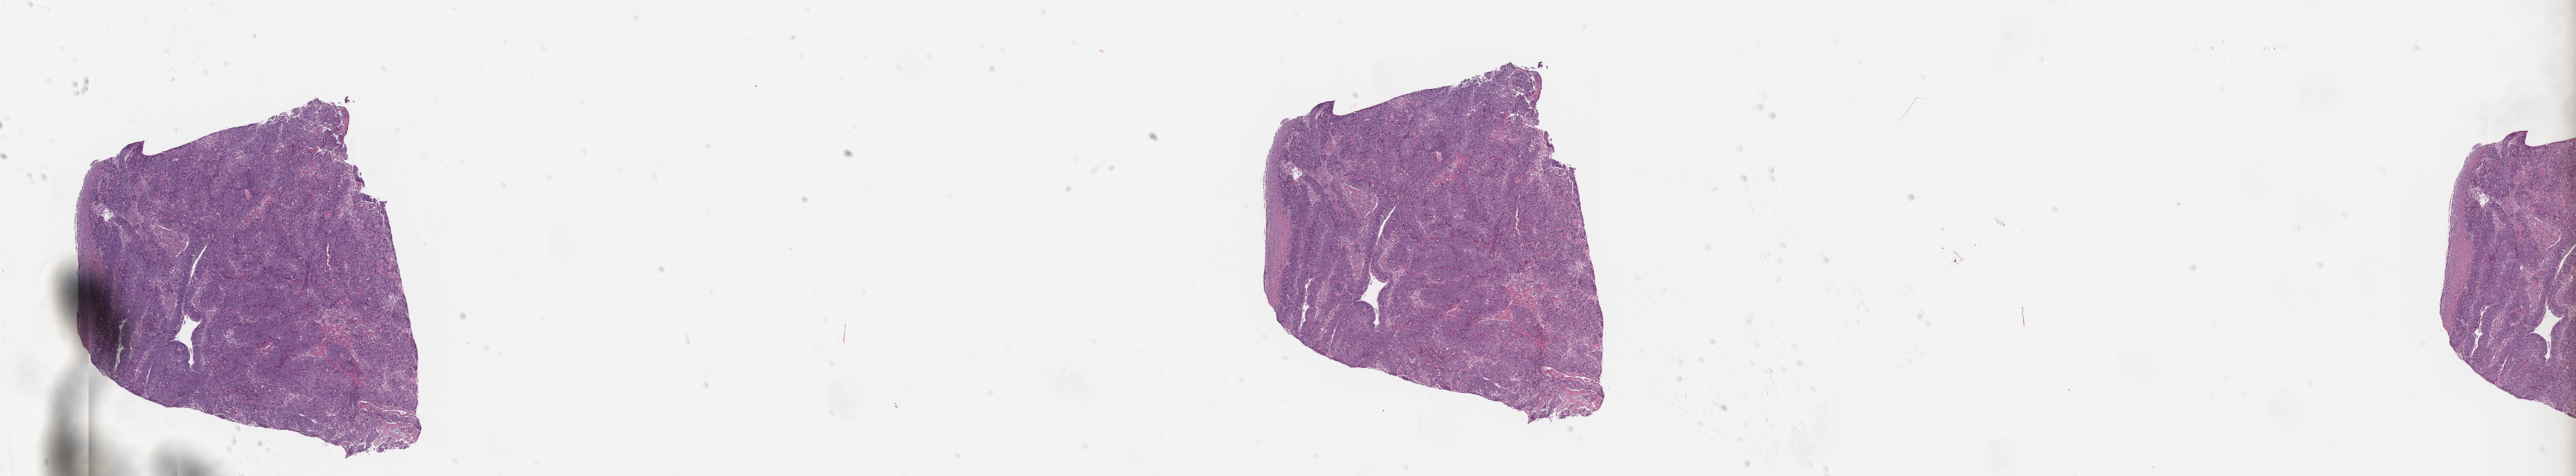
Whole-slide histology image, Hematoxylin and eosin (H&E) stained — shown as a low-resolution overview of the whole scanned area (about 29.0 x 5.4 mm); formalin-fixed paraffin-embedded (FFPE) diagnostic section; primary tumour sample from the uterus. Female patient; age at initial diagnosis 69 years. Histologic grade: G3 (poorly differentiated).
Pathologic diagnosis: Endometrioid adenocarcinoma, NOS (endometrium). FIGO stage: IB.